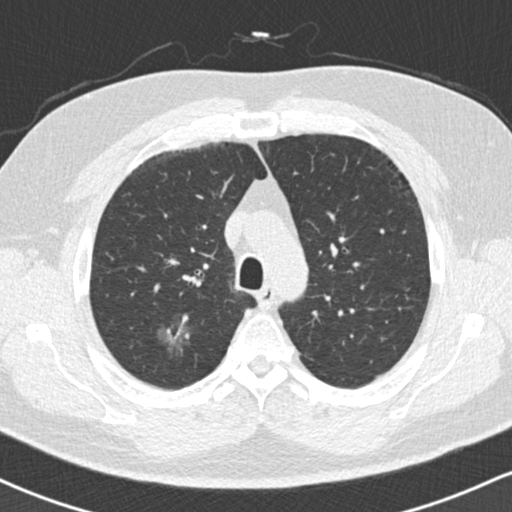
Low-dose screening chest CT, one axial slice; slice 125 of 169 in the series (ordered by position); 120 kVp; lung window (W 1500 / L -600 HU); 512 × 512 image matrix, field of view 320 × 320 mm.
Outlined on this slice (expert manual segmentation):
- lesion 1 (tumor, upper lobe of right lung): box from (x=159, y=325) to (x=190, y=354) px